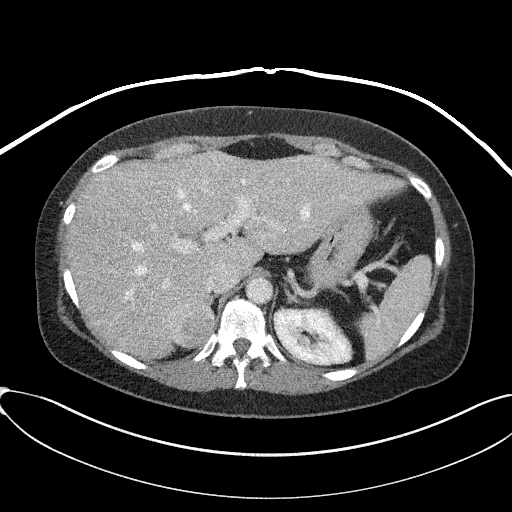
Contrast-enhanced abdominal CT, one axial slice. Slice 62 of 95 in the series (ordered by position). 100 kVp. Intravenous contrast given. Soft-tissue window (W 400 / L 40 HU). 3 mm slice thickness. 512 × 512 image matrix, field of view 410 × 410 mm. Female patient, age 46 years. From the clinical record (not read from this slice): diagnosis: adrenocortical carcinoma; tumour side: right adrenal; tumour size at pathology: 7.2 cm.
Annotated regions visible in this slice (semi-automatically segmented with operator editing):
- mass: box from (x=165, y=296) to (x=214, y=346) px